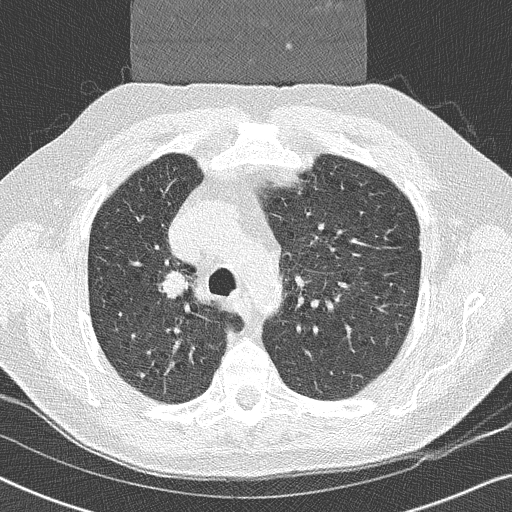
Chest CT (low-dose screening protocol), one axial image; second screening round (one year after baseline); lung window (W 1500 / L -600 HU); 120 kVp; slice 79 of 252 in the series. Male, age 59 years at enrolment. Former smoker at enrolment.
- Expert reader's lesion annotation, bounding box [x1, y1, x2, y2] px = [142, 256, 203, 308].
- Reader record for this screening exam (exam-level; its link to the box is not recorded): non-calcified nodule or mass ≥4 mm, right upper lobe, 17 × 16 mm, smooth margins, soft tissue attenuation, pre-existing on the prior screen: yes.
- Lung cancer was diagnosed 14 days after this screen: squamous cell carcinoma, NOS, right upper lobe, poorly differentiated (G3), stage IIA (AJCC 6th edition), 20 mm at pathology.